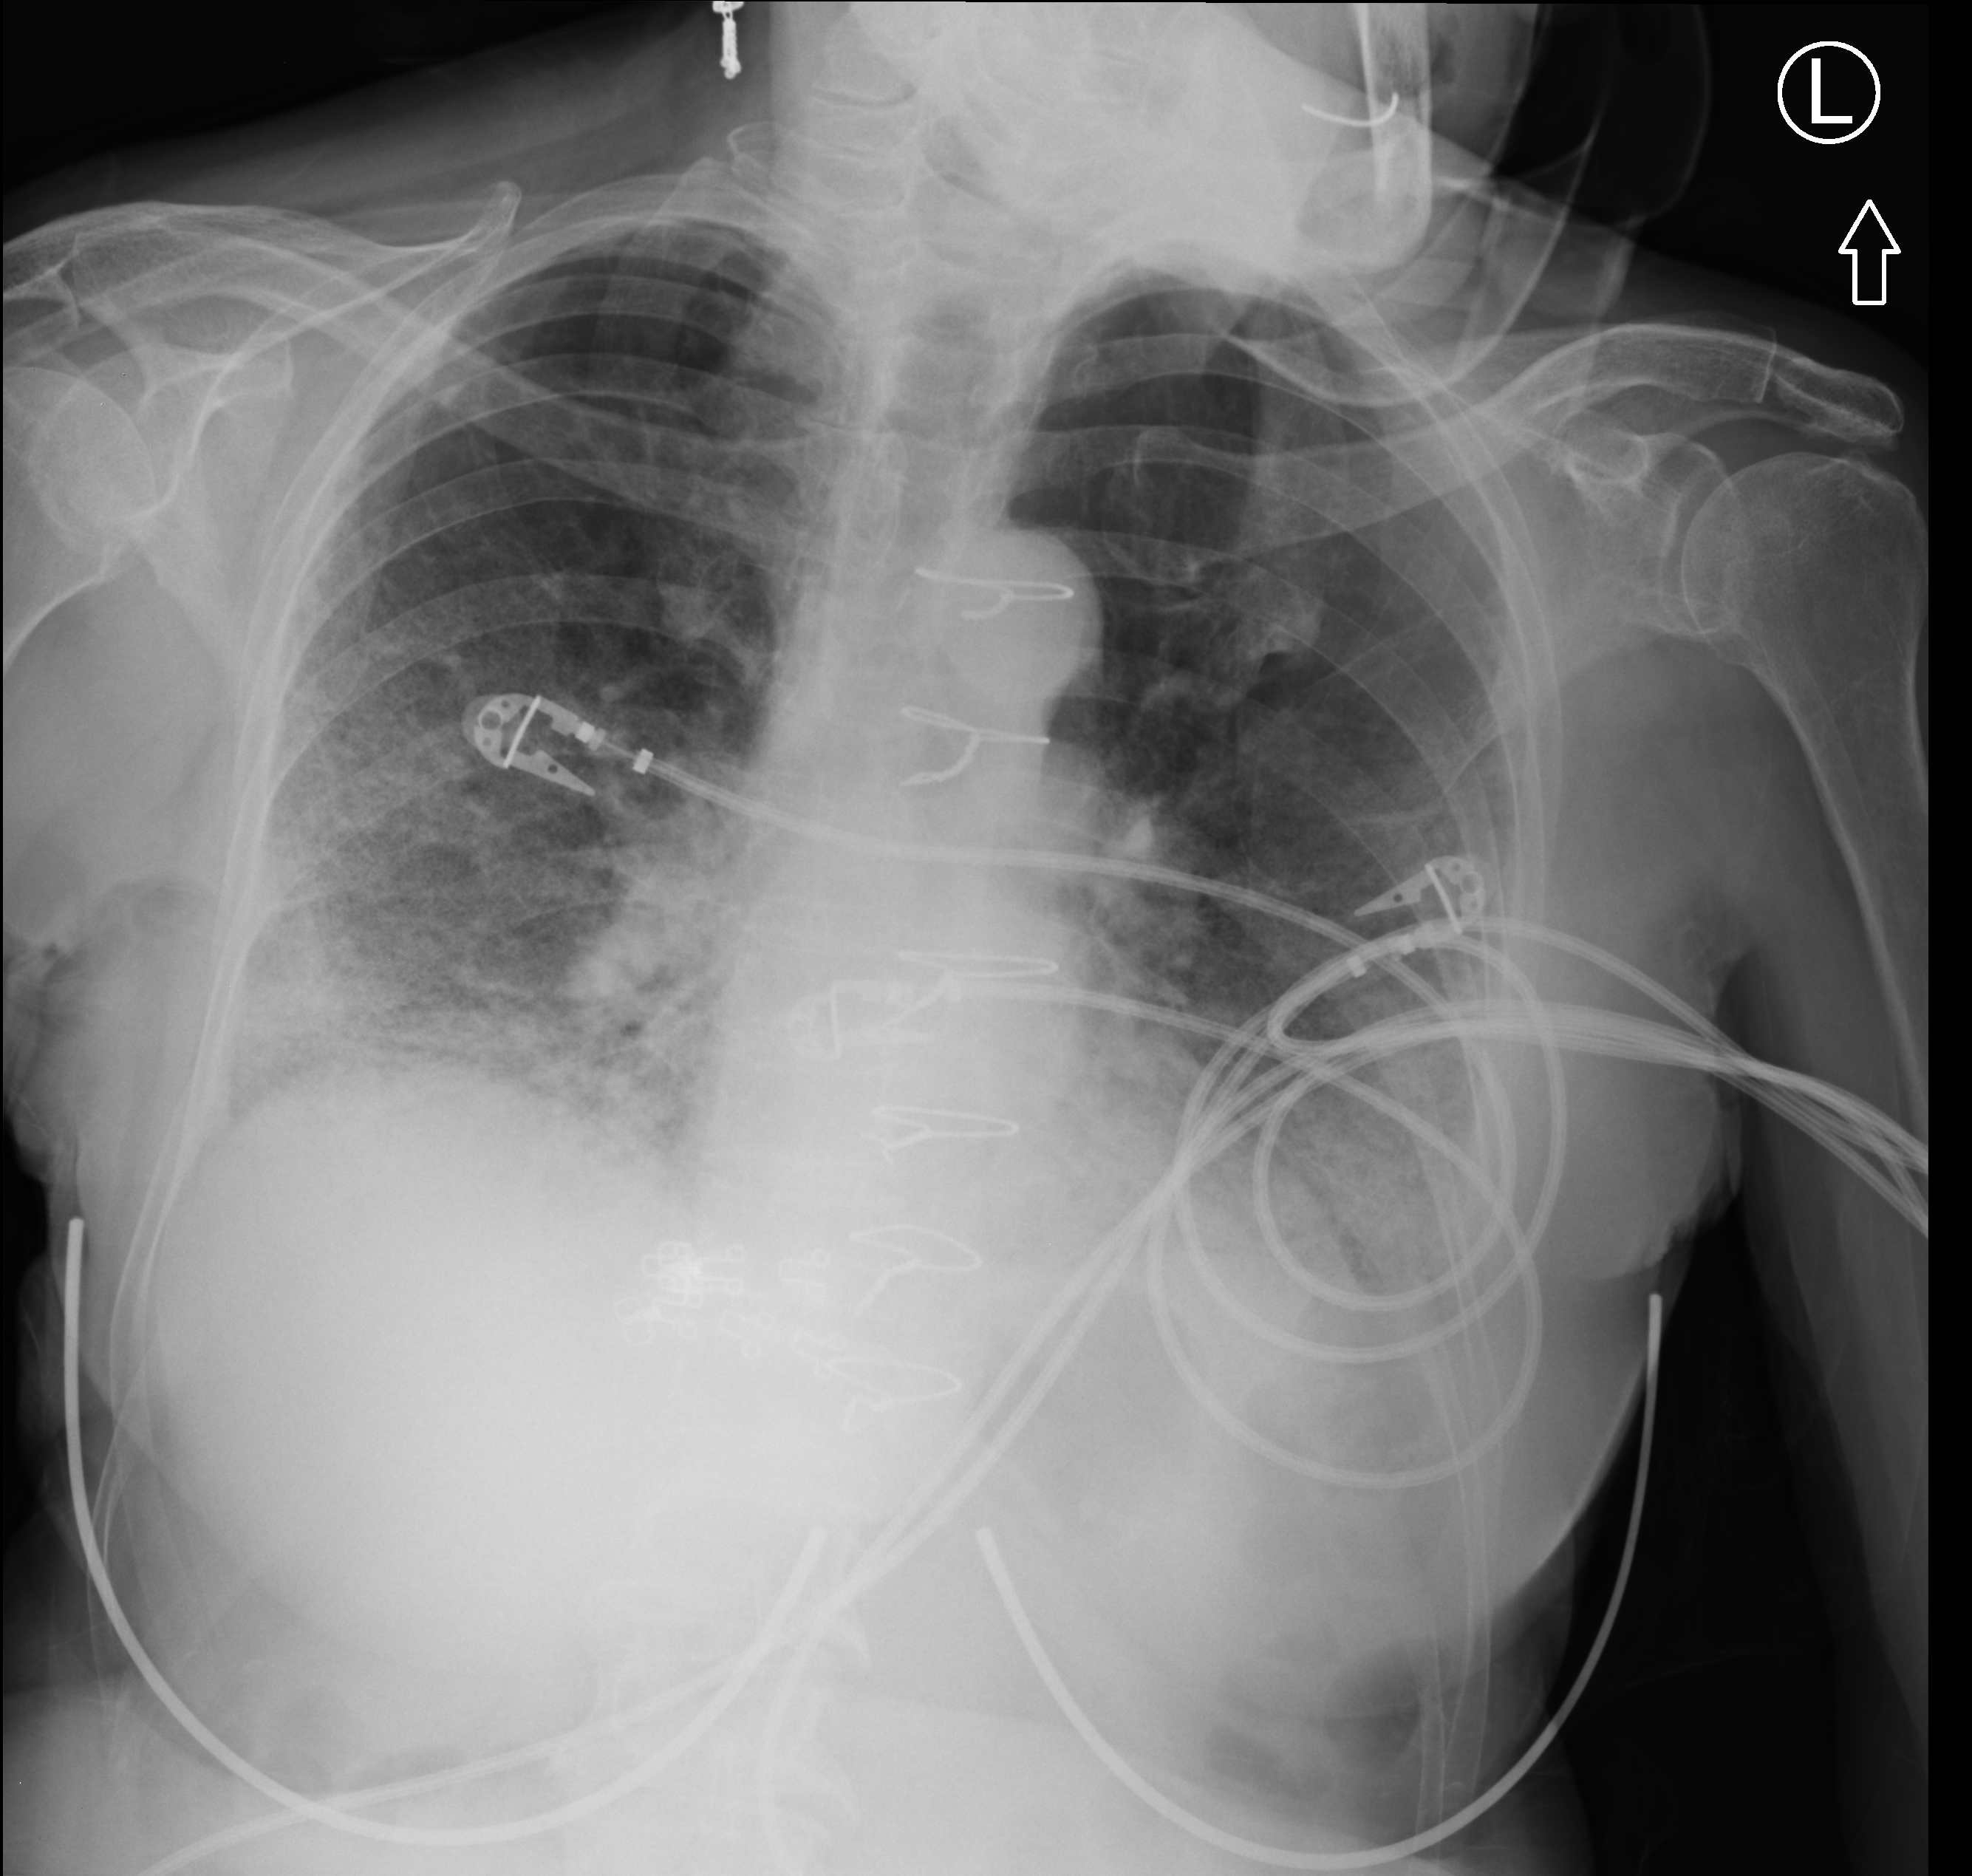
Bedside chest radiograph (computed radiography), anteroposterior (AP) projection. Female patient hospitalised with COVID-19, age 75–90 years.
Admission-level facts for this patient (not findings on this image; timing relative to this image not recorded): admitted to intensive care during this hospital stay: no.